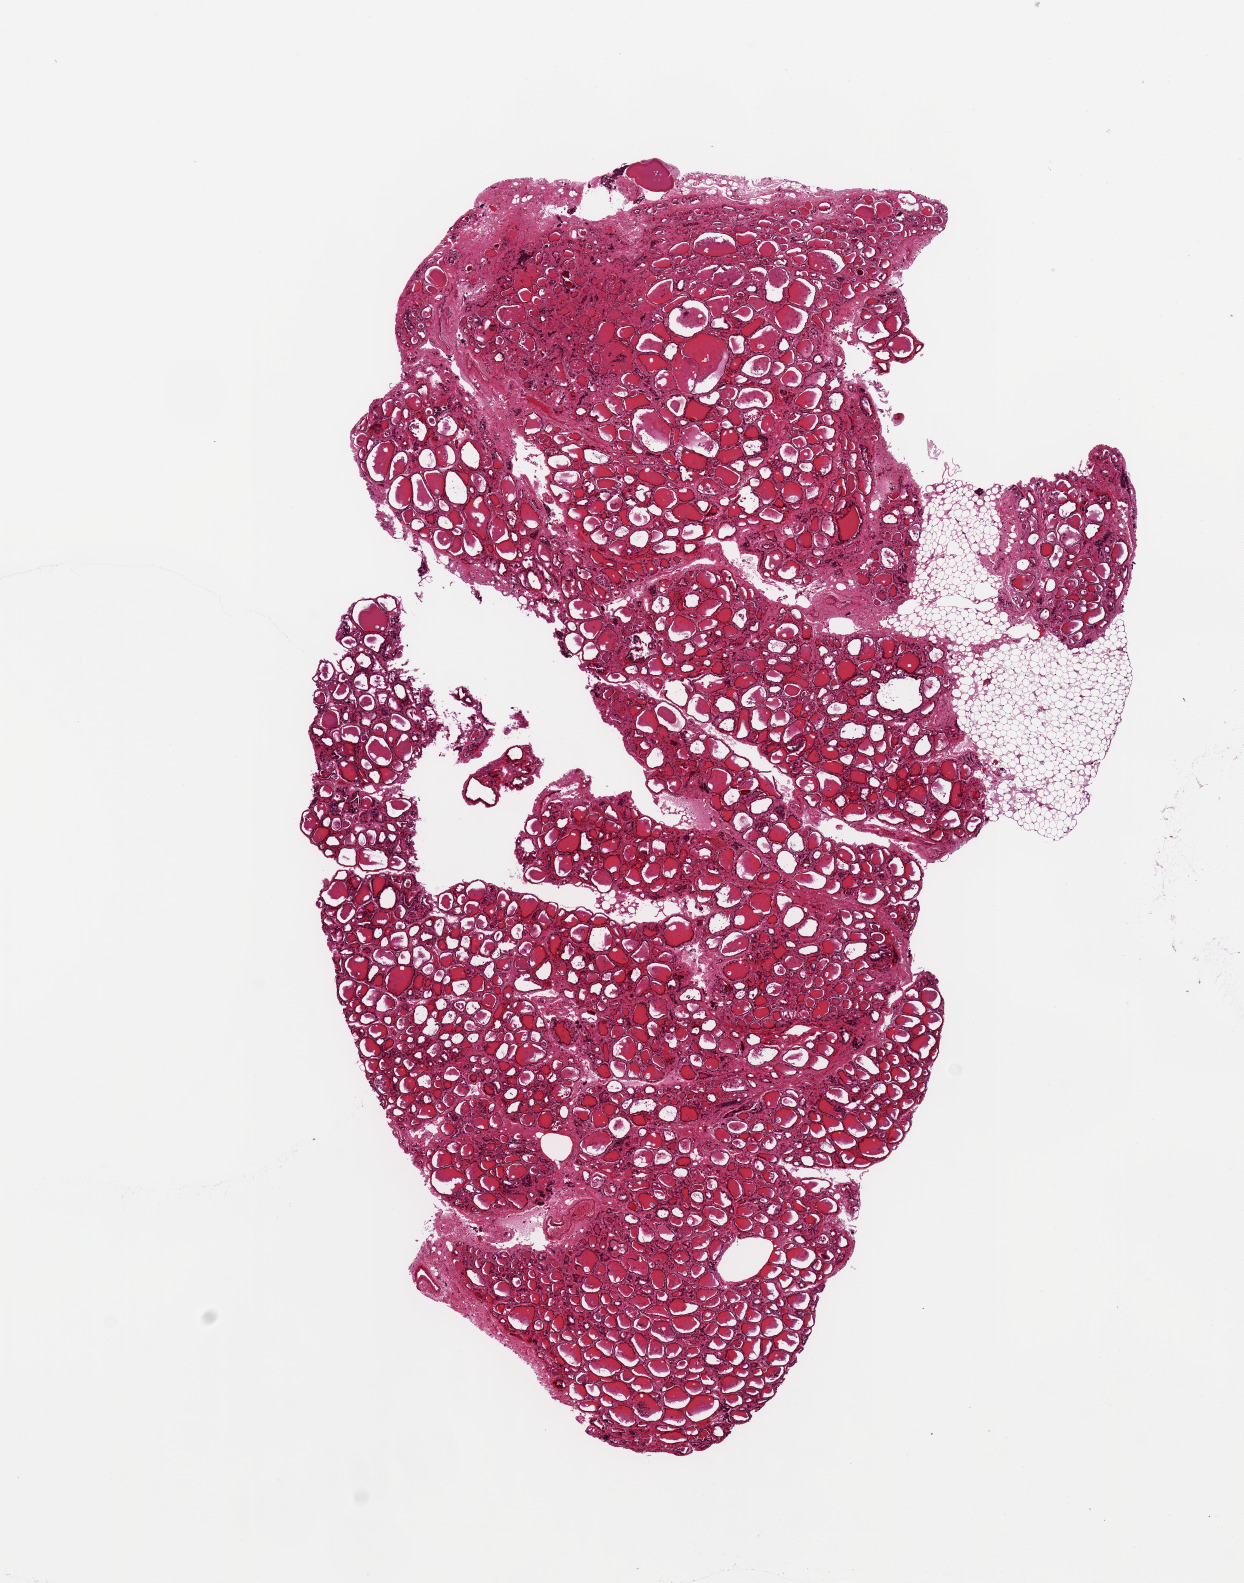
Whole-slide image, haematoxylin and eosin stain, shown as a low-resolution overview of the whole scanned area (about 9.8 x 12.5 mm). PAXgene-fixed paraffin-embedded (PFPE) section. Section of thyroid (target tissue). Donor tissue sample. Donor sex: male.
• review note (as recorded): 10x6.3mm